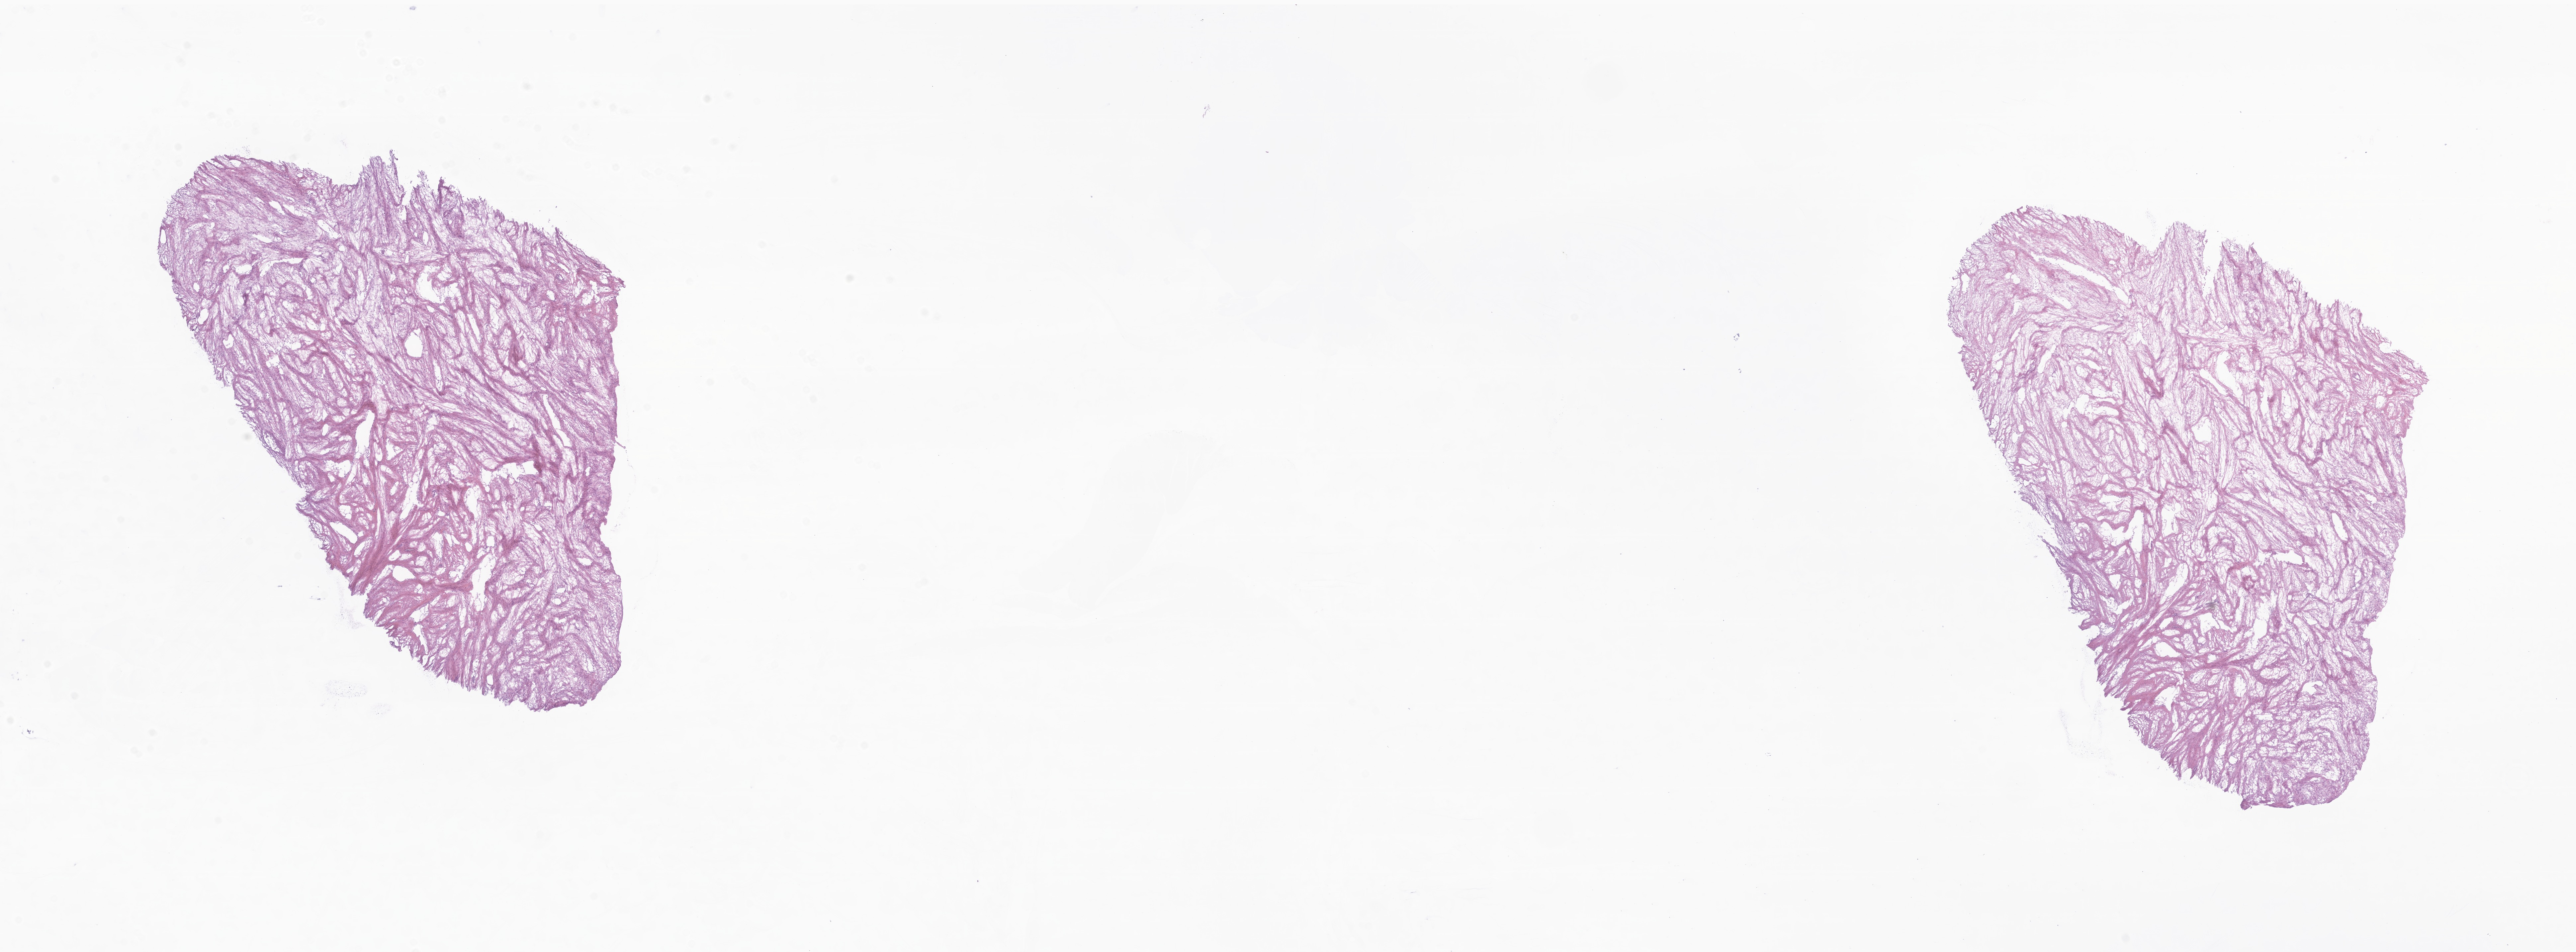
Haematoxylin and eosin whole-slide image of tumor tissue from the retroperitoneum, whole scanned area (about 32.7 x 12.1 mm) shown as a low-resolution overview. Frozen section (OCT-embedded). Patient: female, age 203 months (16 years 11 months).
Diagnosis: Aggressive fibromatosis.